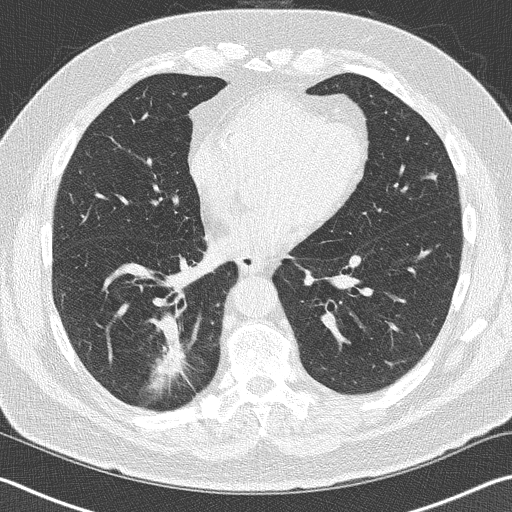
Axial slice from a low-dose chest CT screening exam. Baseline screening round. Lung window (W 1500 / L -600 HU). Lung (sharp) reconstruction kernel (B50f). Slice 96 of 141 in the series. Male, age 70 years at enrolment. Current smoker at enrolment.
Expert reader's lesion annotation, bounding box <138,332,214,403> (left, top, right, bottom; pixels). Reader record for this screening exam (exam-level; its link to the box is not recorded): non-calcified nodule or mass ≥4 mm, right lower lobe, 28 × 23 mm, spiculated (stellate) margins, soft tissue attenuation. Lung cancer was diagnosed 62 days after this screen: squamous cell carcinoma, NOS, right lower lobe, poorly differentiated (G3), stage IB (AJCC 6th edition), 24 mm at pathology.